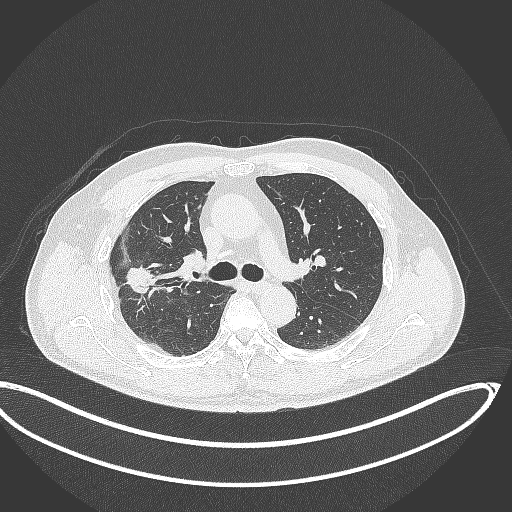
Chest CT, one axial slice. Slice 221 of 391 in the series (ordered by position). 120 kVp. Lung window (W 1500 / L -600 HU). 1 mm slice thickness. 512 × 512 image matrix, field of view 439 × 439 mm. Male patient, age 63 years. Case-level facts recorded for this patient, not image findings: clinical TNM (as recorded): T1c N0 M0.
Structures marked on this image (rectangle marked by the reading radiologist):
- lung tumour (recorded histology: adenocarcinoma): bounding box [x1, y1, x2, y2] px = [120, 261, 160, 305]